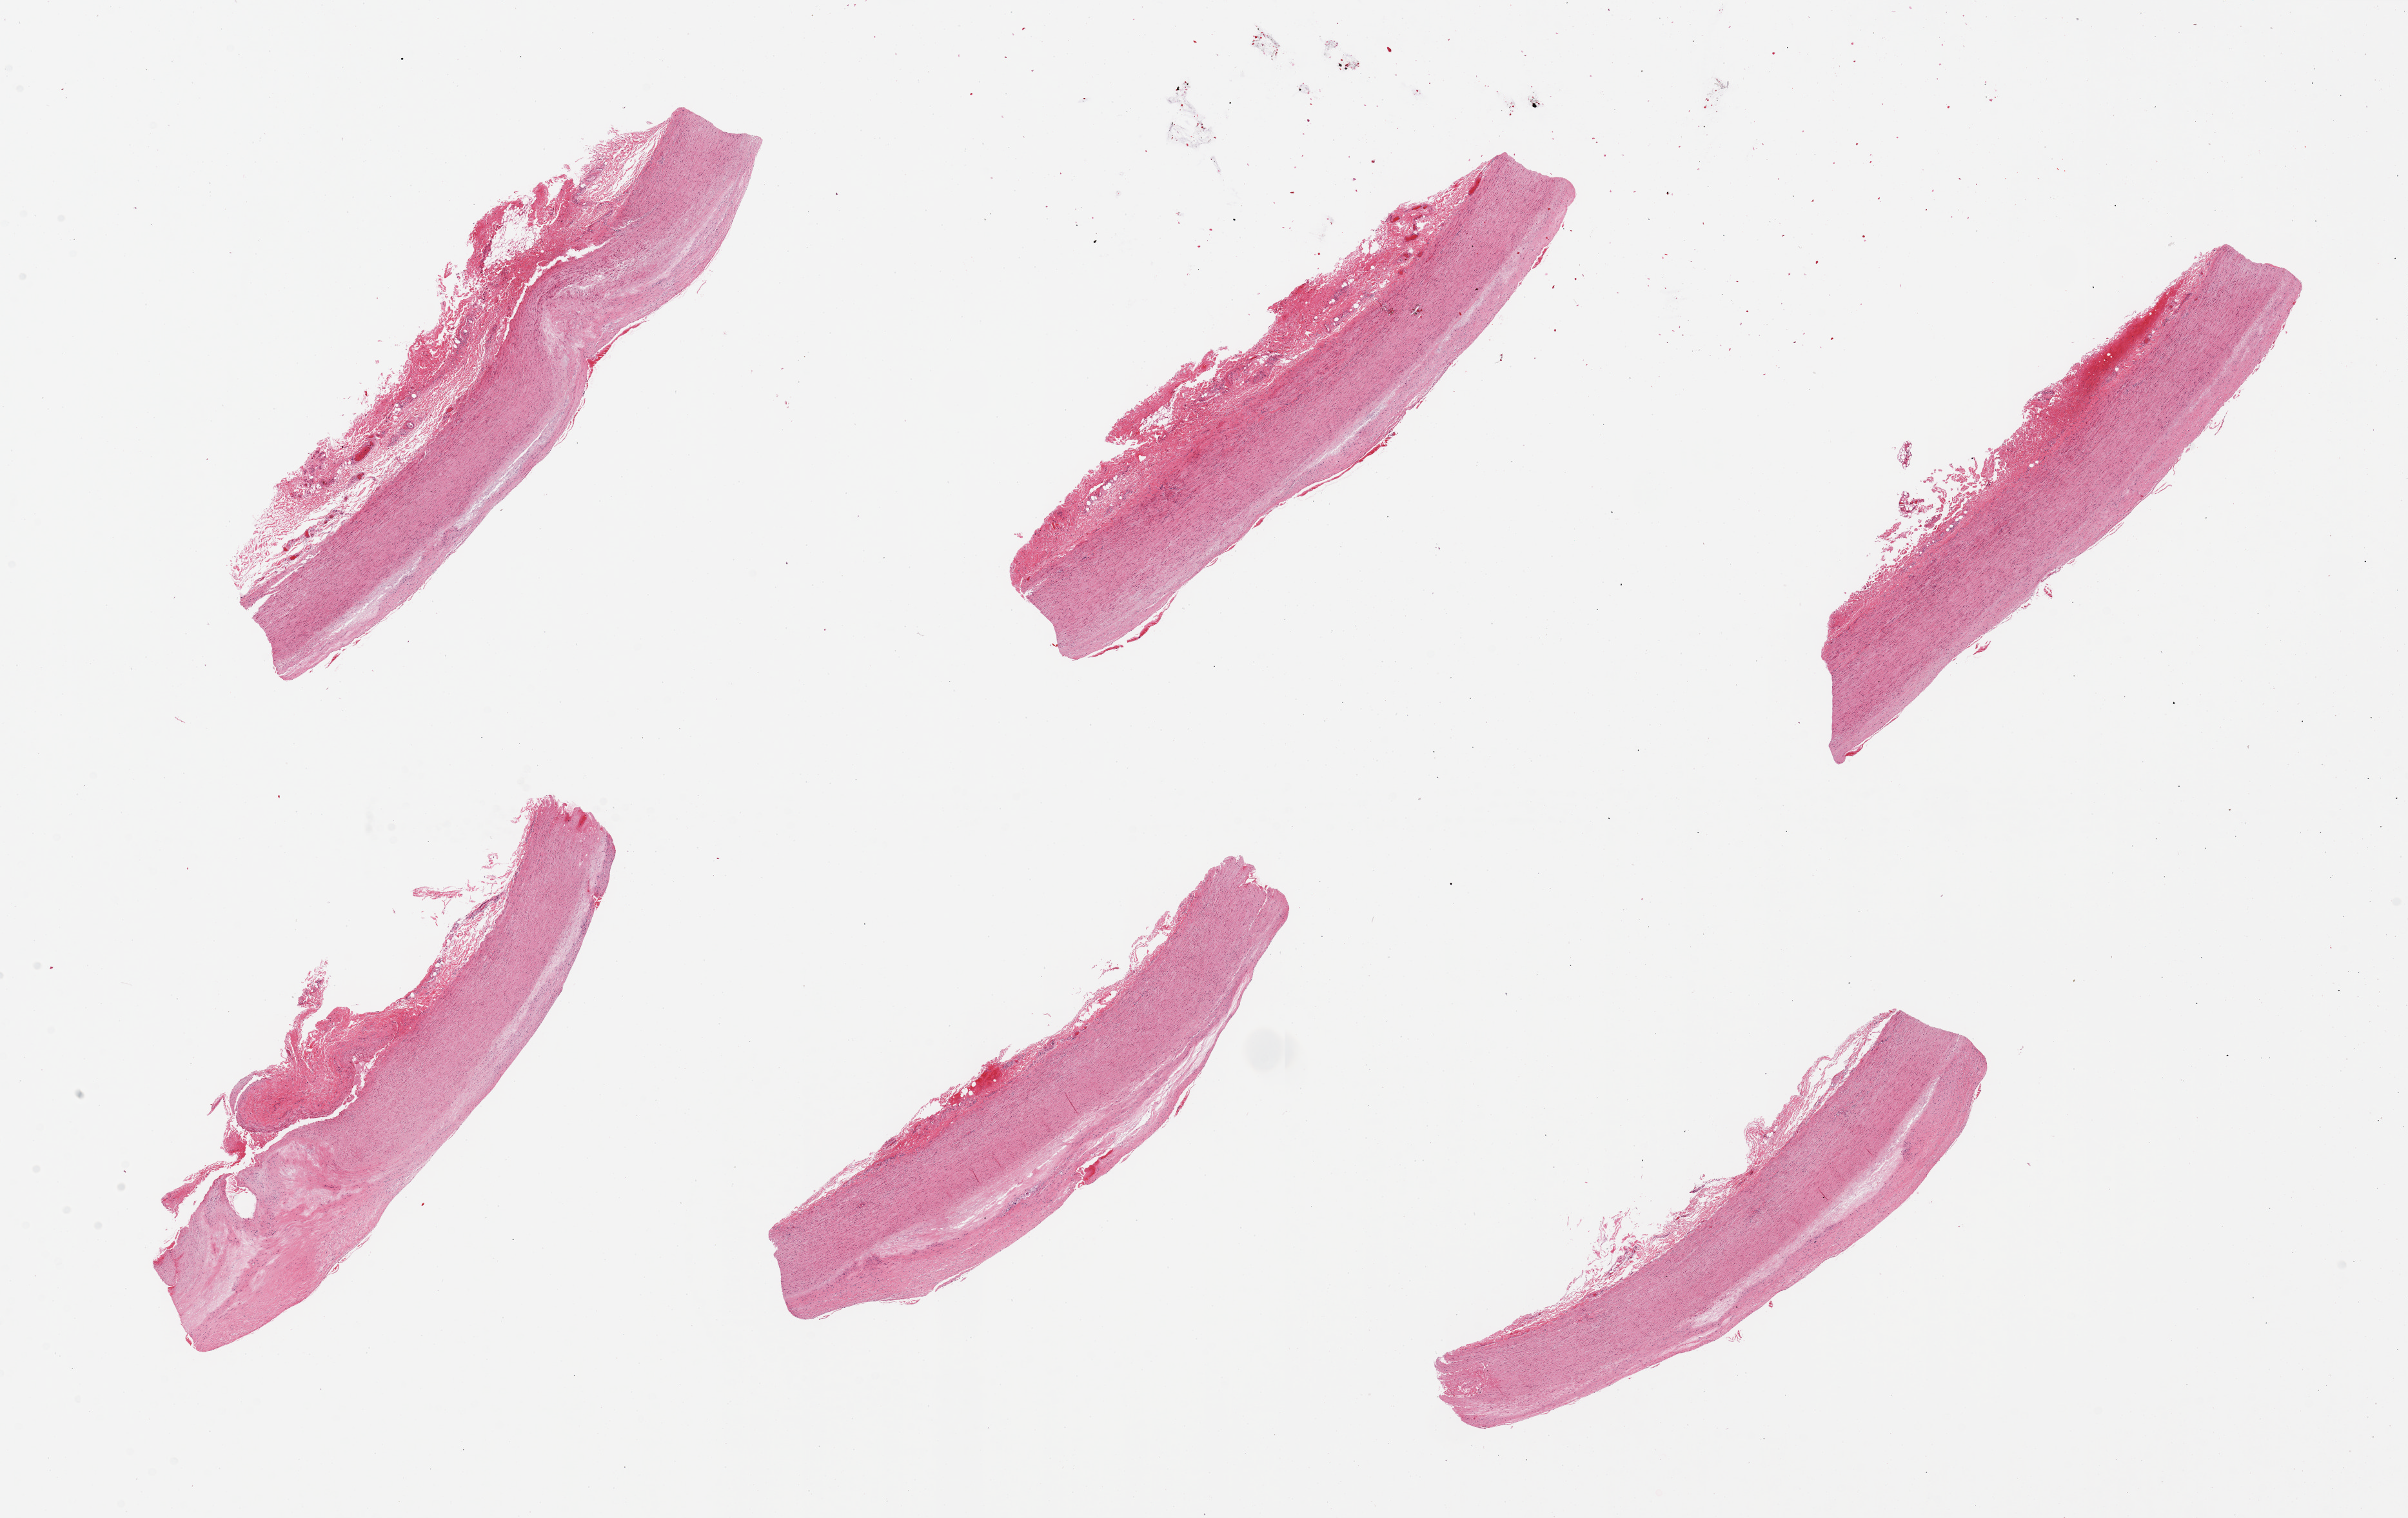
Digitized H&E-stained section, brightfield, whole scanned area (about 29.5 x 18.6 mm, from a 20x scan) shown as a low-resolution overview; PAXgene-fixed paraffin-embedded (PFPE) section; section of aorta (target tissue); tissue donor sample. Donor sex: male.
Review note (as recorded): 6 pieces; atherosclerosis.